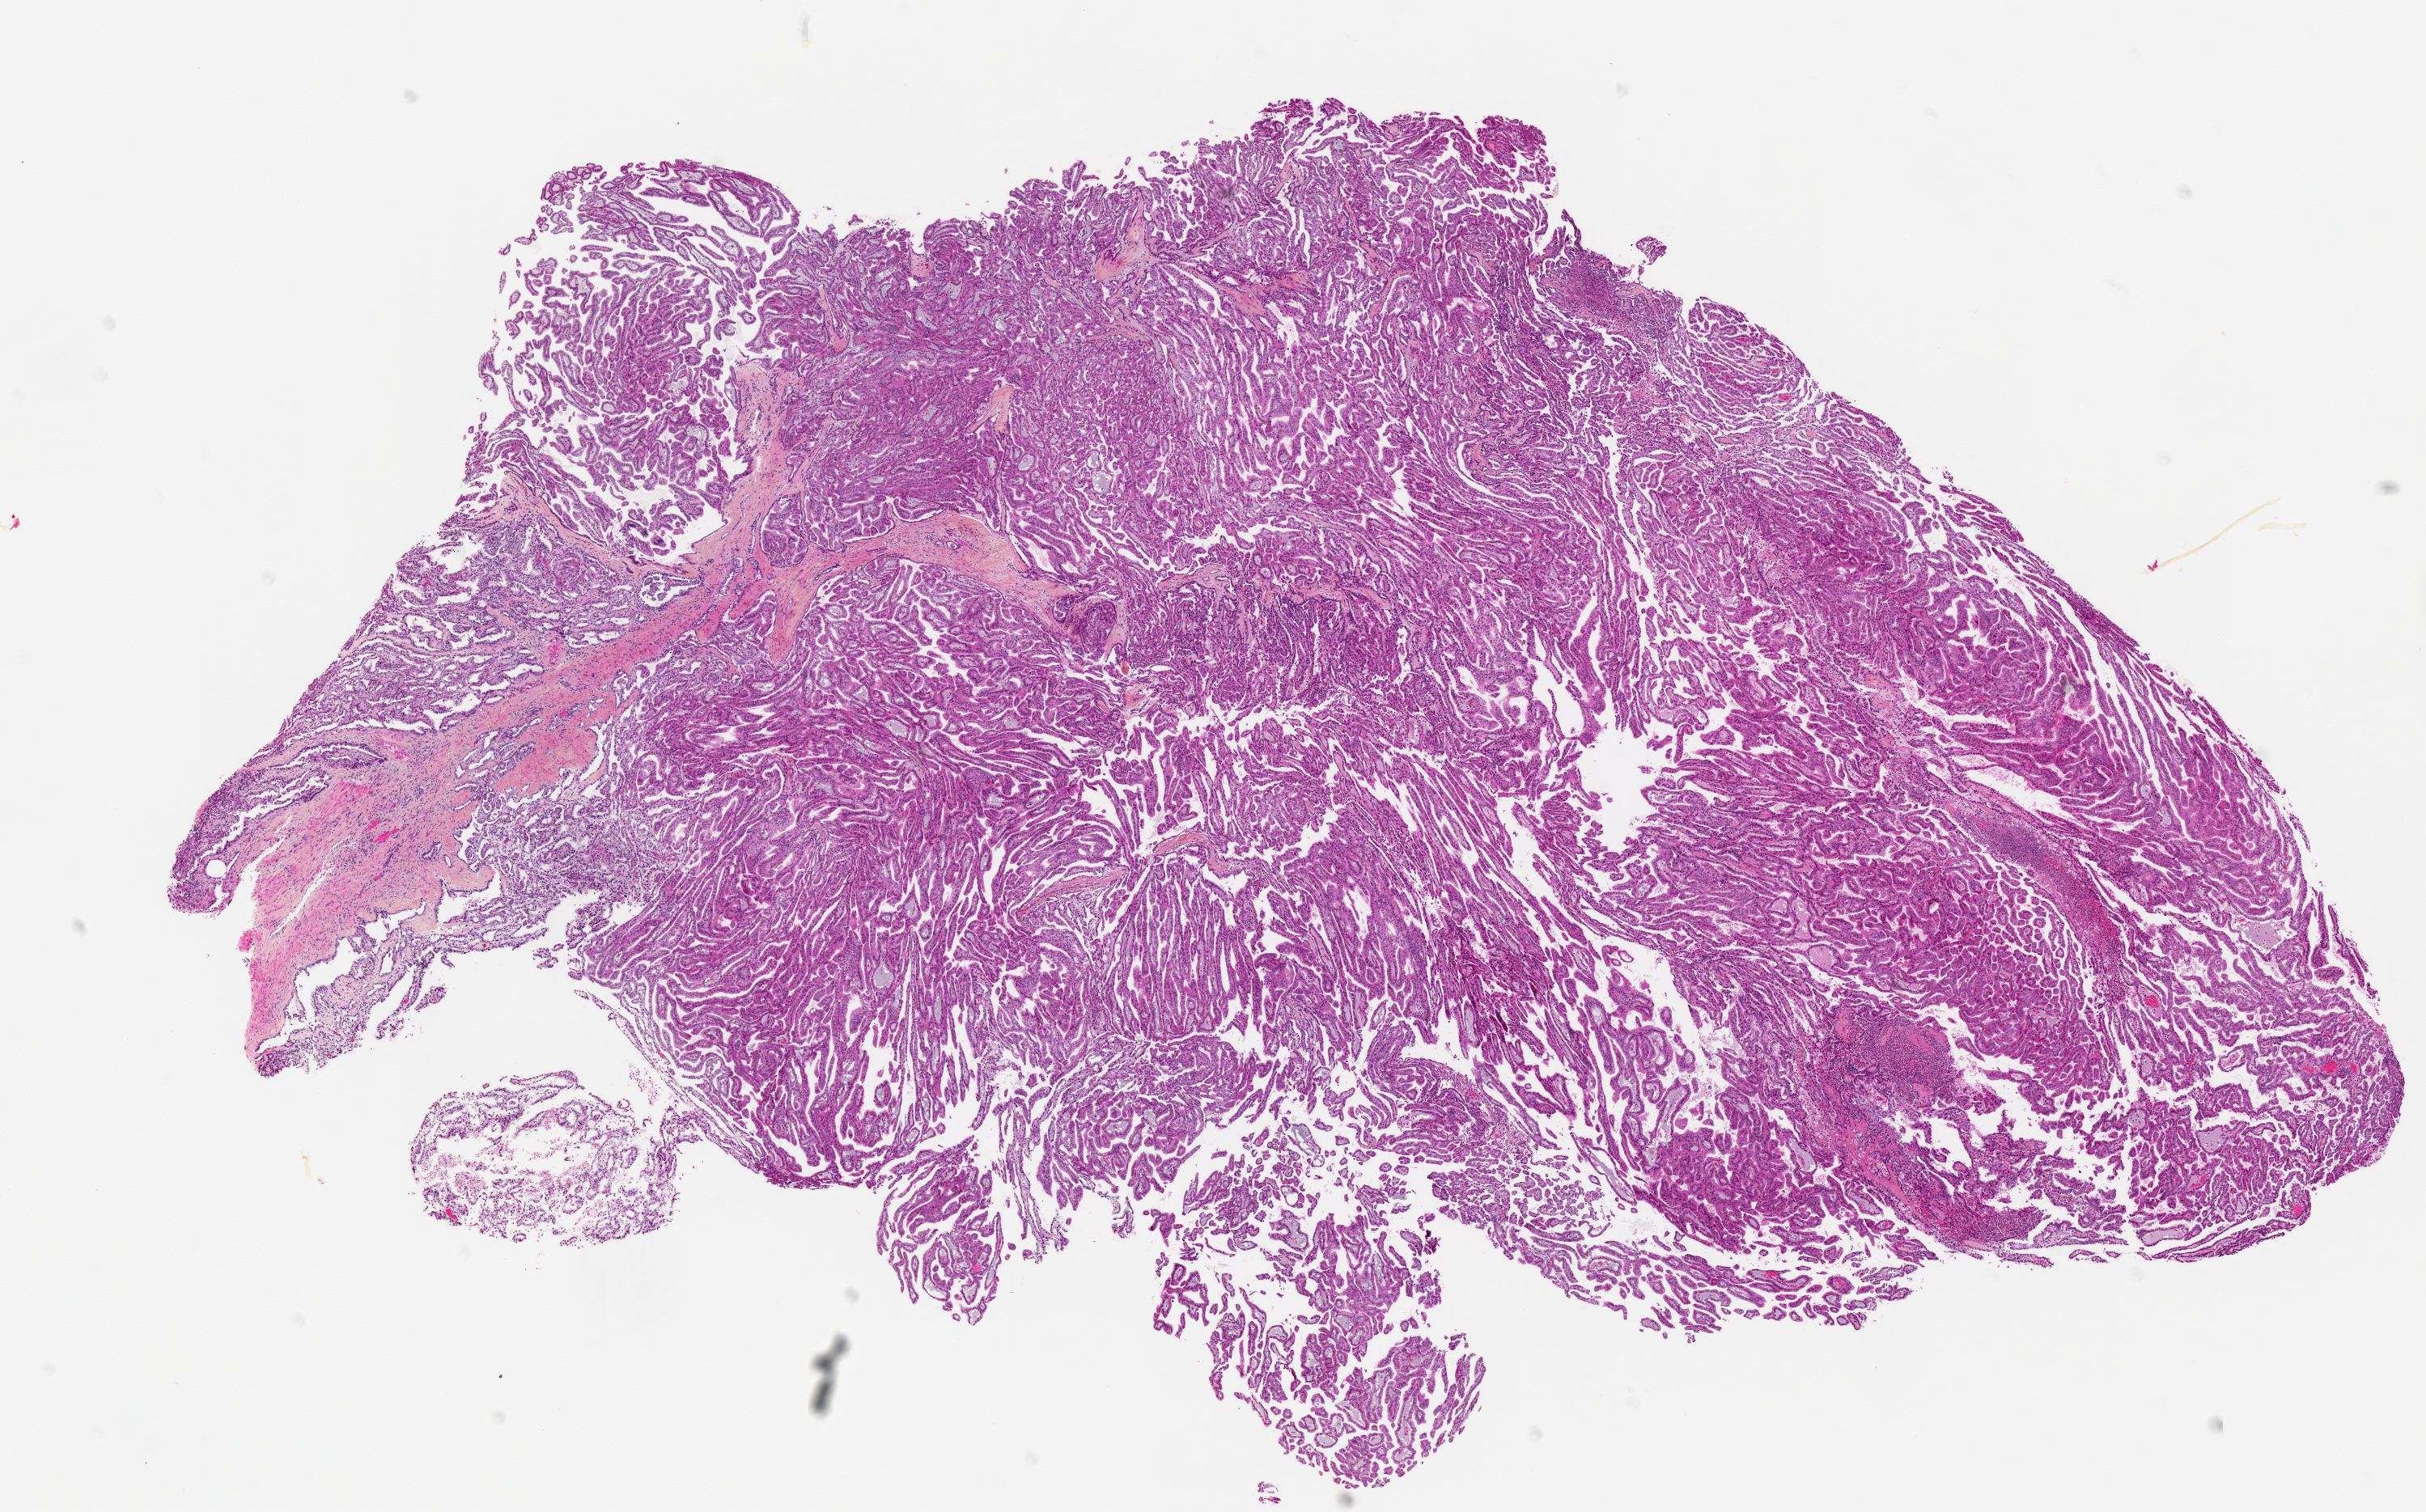
Whole-slide histology image, H&E-stained, low-resolution overview of the scanned area, about 12.0 x 7.5 mm (acquisition: 20x scan), formalin-fixed paraffin-embedded (FFPE) diagnostic section, kidney, primary tumour sample. Male, age 58 years at initial diagnosis.
Diagnosis: Papillary adenocarcinoma, NOS.